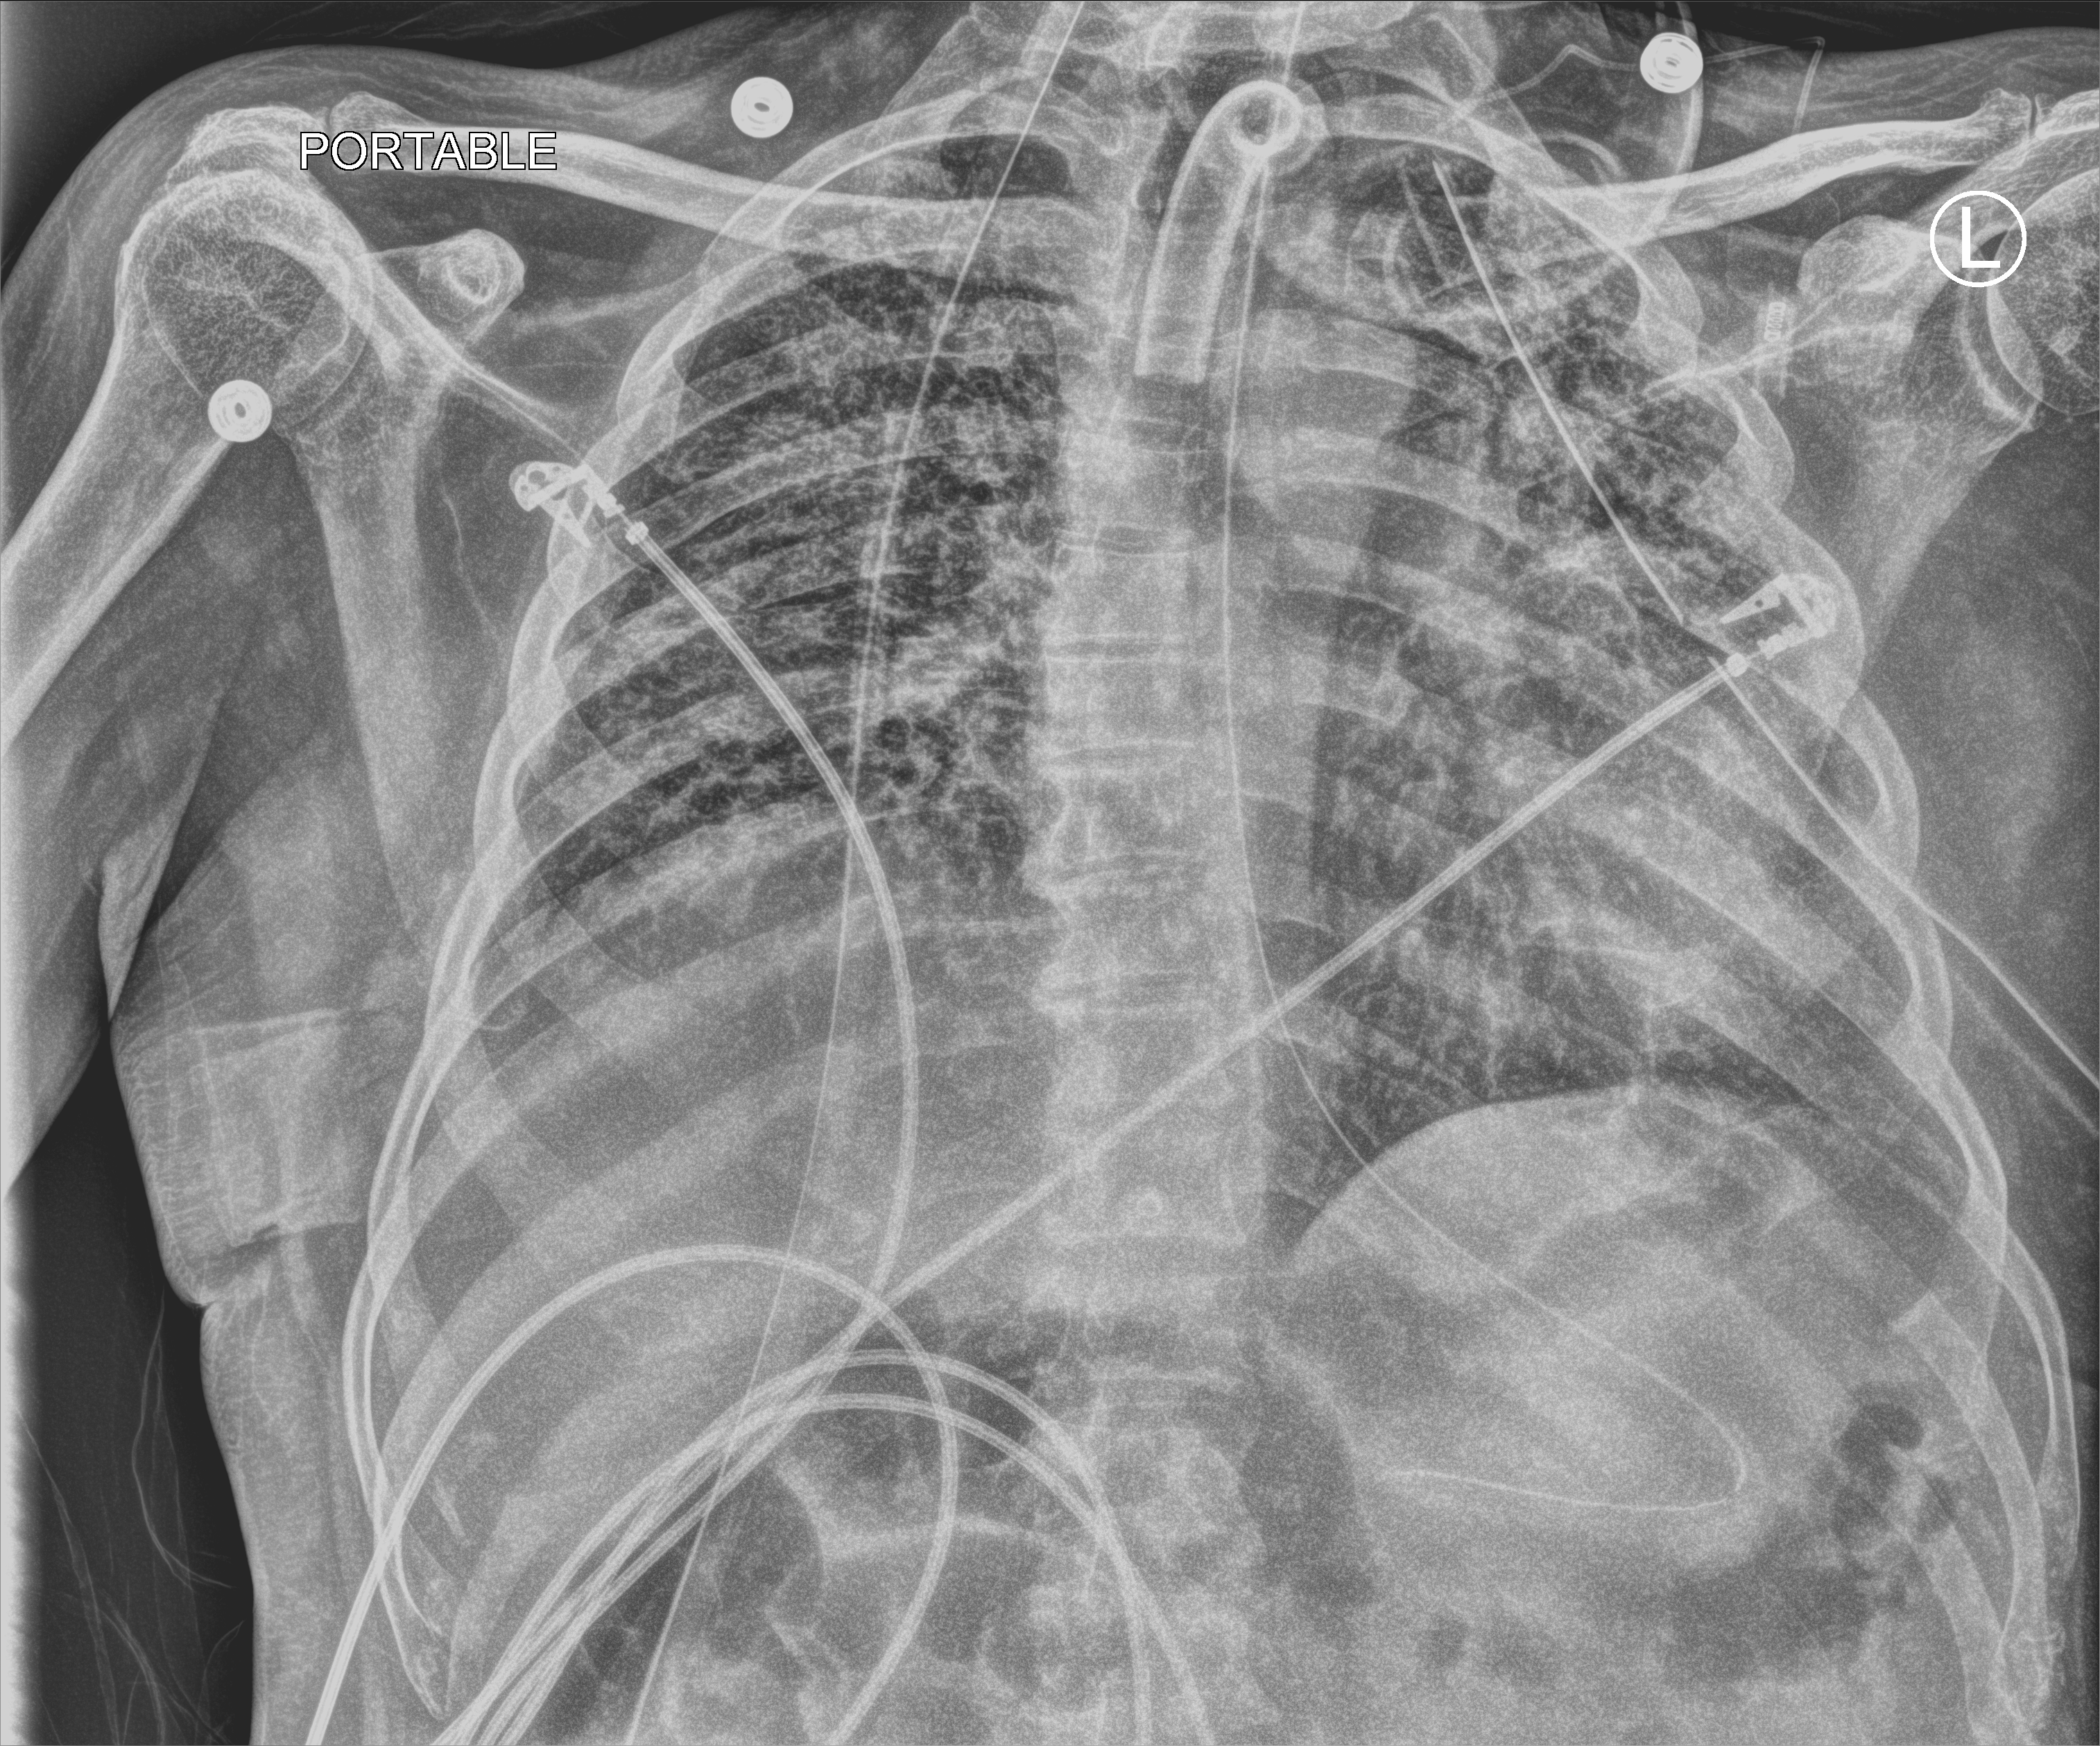
Bedside chest radiograph (computed radiography). Male patient hospitalised with COVID-19, age 18–59 years.
From the hospital-stay record, not from the radiograph (when in the stay this image was taken is not recorded): admitted to intensive care during this hospital stay: yes.